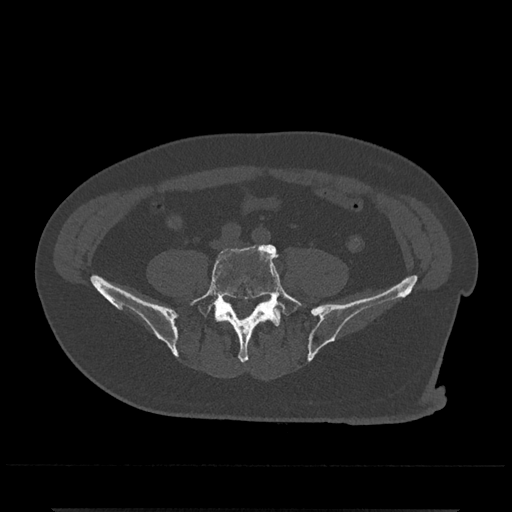
CT including the spine, one axial slice; slice 87 of 797 in the series (ordered by position); bone window (W 1800 / L 400 HU); 0.5 mm slice thickness; 512 × 512 image matrix. Male patient, age 67 years. Case-level facts recorded for this patient, not image findings: primary cancer: prostate.
Annotated regions visible in this slice (semi-automatic segmentation, software-assisted and operator-edited):
- L5 vertebra: bounding box [x1, y1, x2, y2] px = [188, 244, 307, 363]